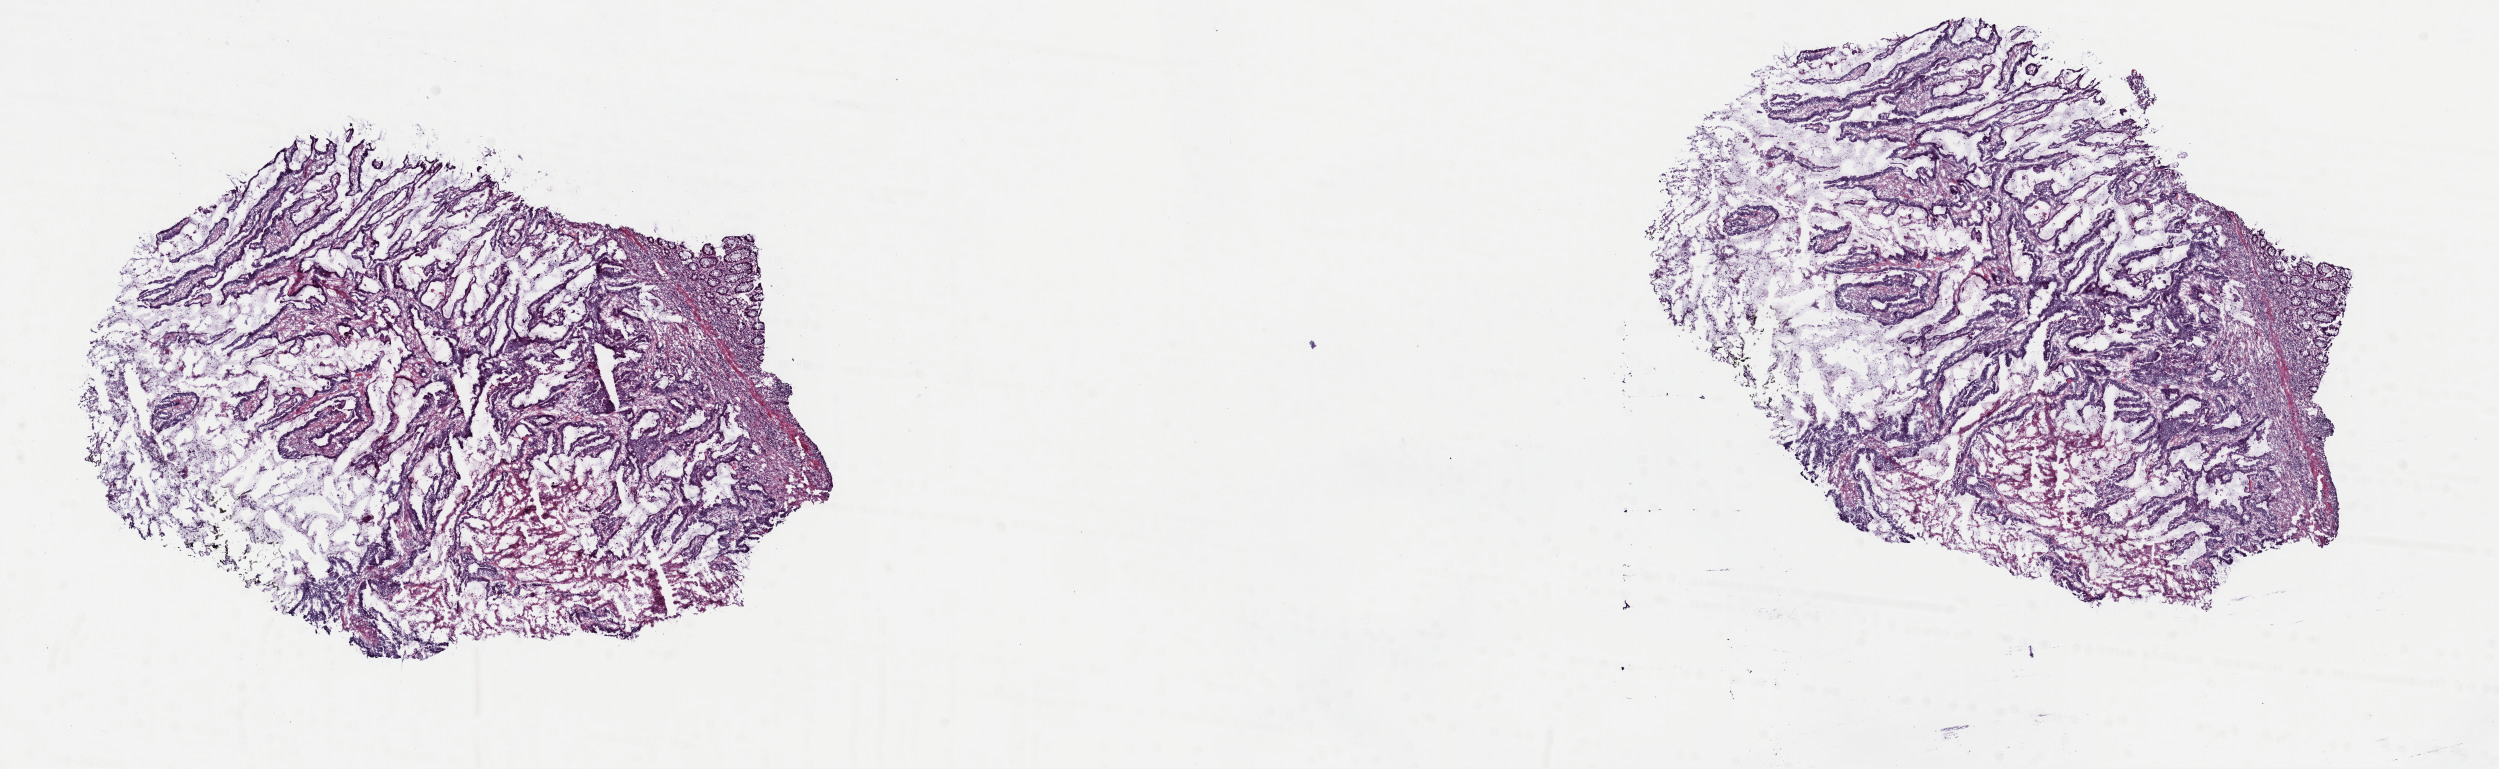
Whole-slide histology image, H&E, shown as a low-resolution overview of the whole scanned area (about 19.7 x 6.1 mm, acquisition: 40x scan). Frozen section. Primary tumour sample from the colon. Patient: female, age at initial diagnosis 74 years. Slide review estimates, as recorded: tumour cells 90%, tumour nuclei 65%, normal cells 5%, stromal cells 0%, necrosis 5%. Inflammatory infiltration, as recorded: lymphocyte infiltration 5%, monocyte infiltration 1%, neutrophil infiltration 0%.
Diagnosis: Adenocarcinoma, NOS (cecum). TNM: T3 N0 MX. AJCC pathologic stage: IIA.